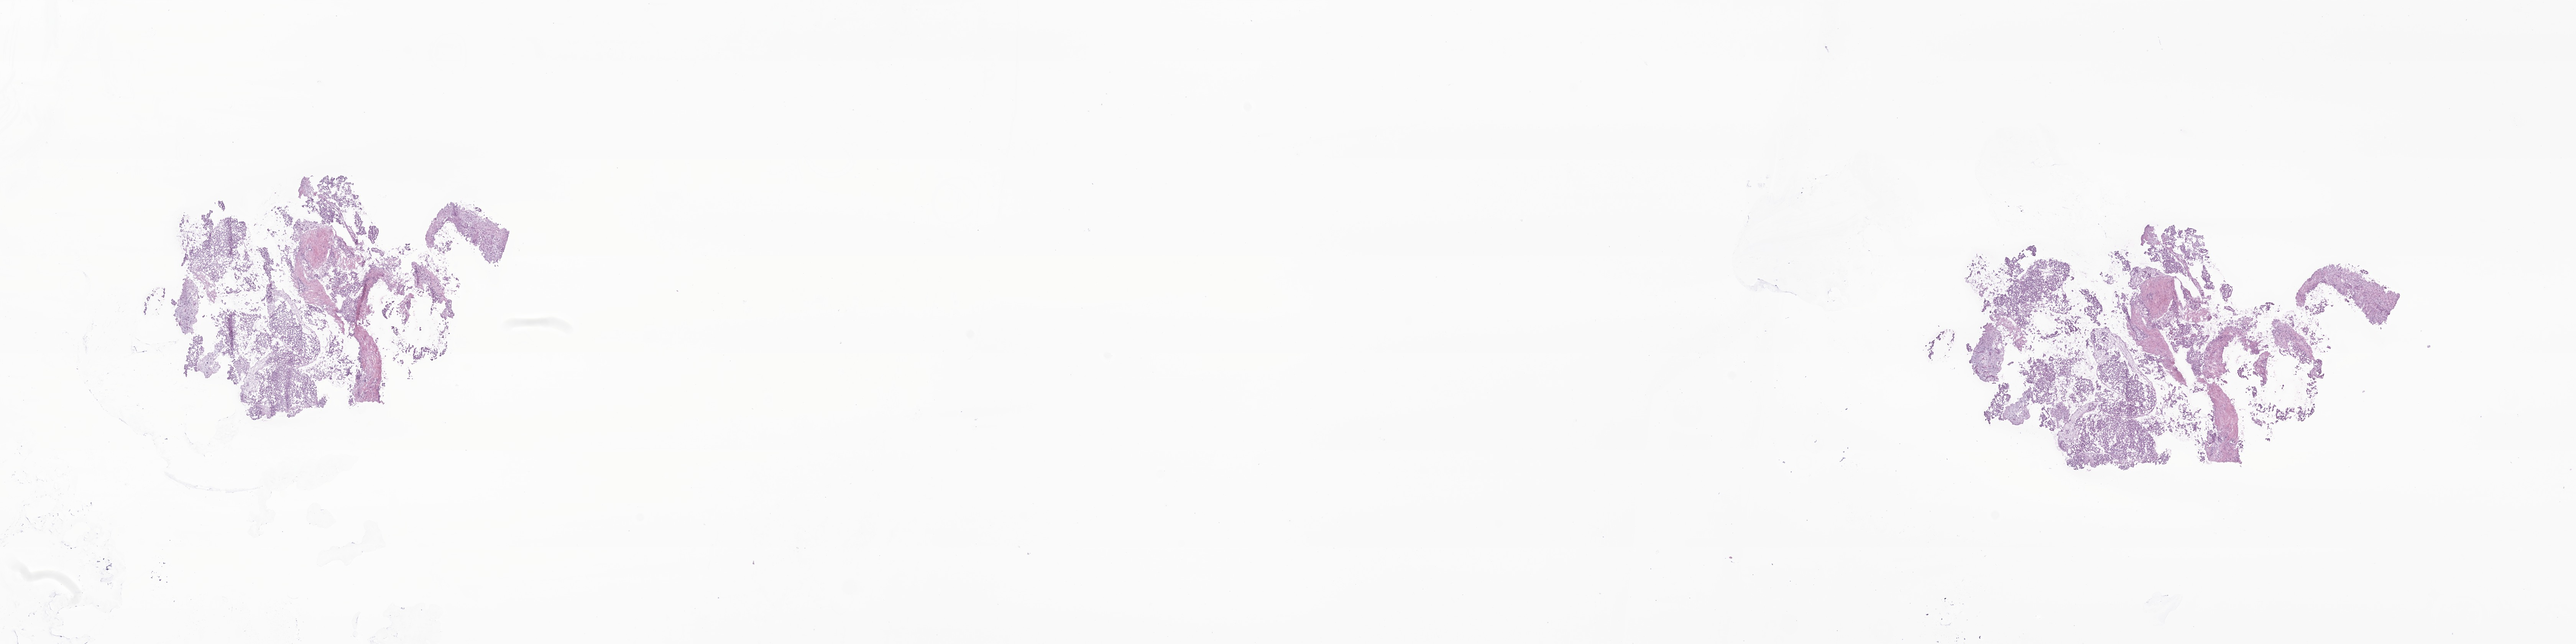
Digitized haematoxylin and eosin-stained section of tumor tissue from the tail of pancreas, a low-resolution overview of the entire scanned area, about 28.3 x 7.1 mm; cryosection (OCT / tissue freezing medium). Male patient, age 137 months (11 years 5 months).
Diagnosis (ICD-O-3 morphology term): Adenocarcinoma, metastatic, NOS.